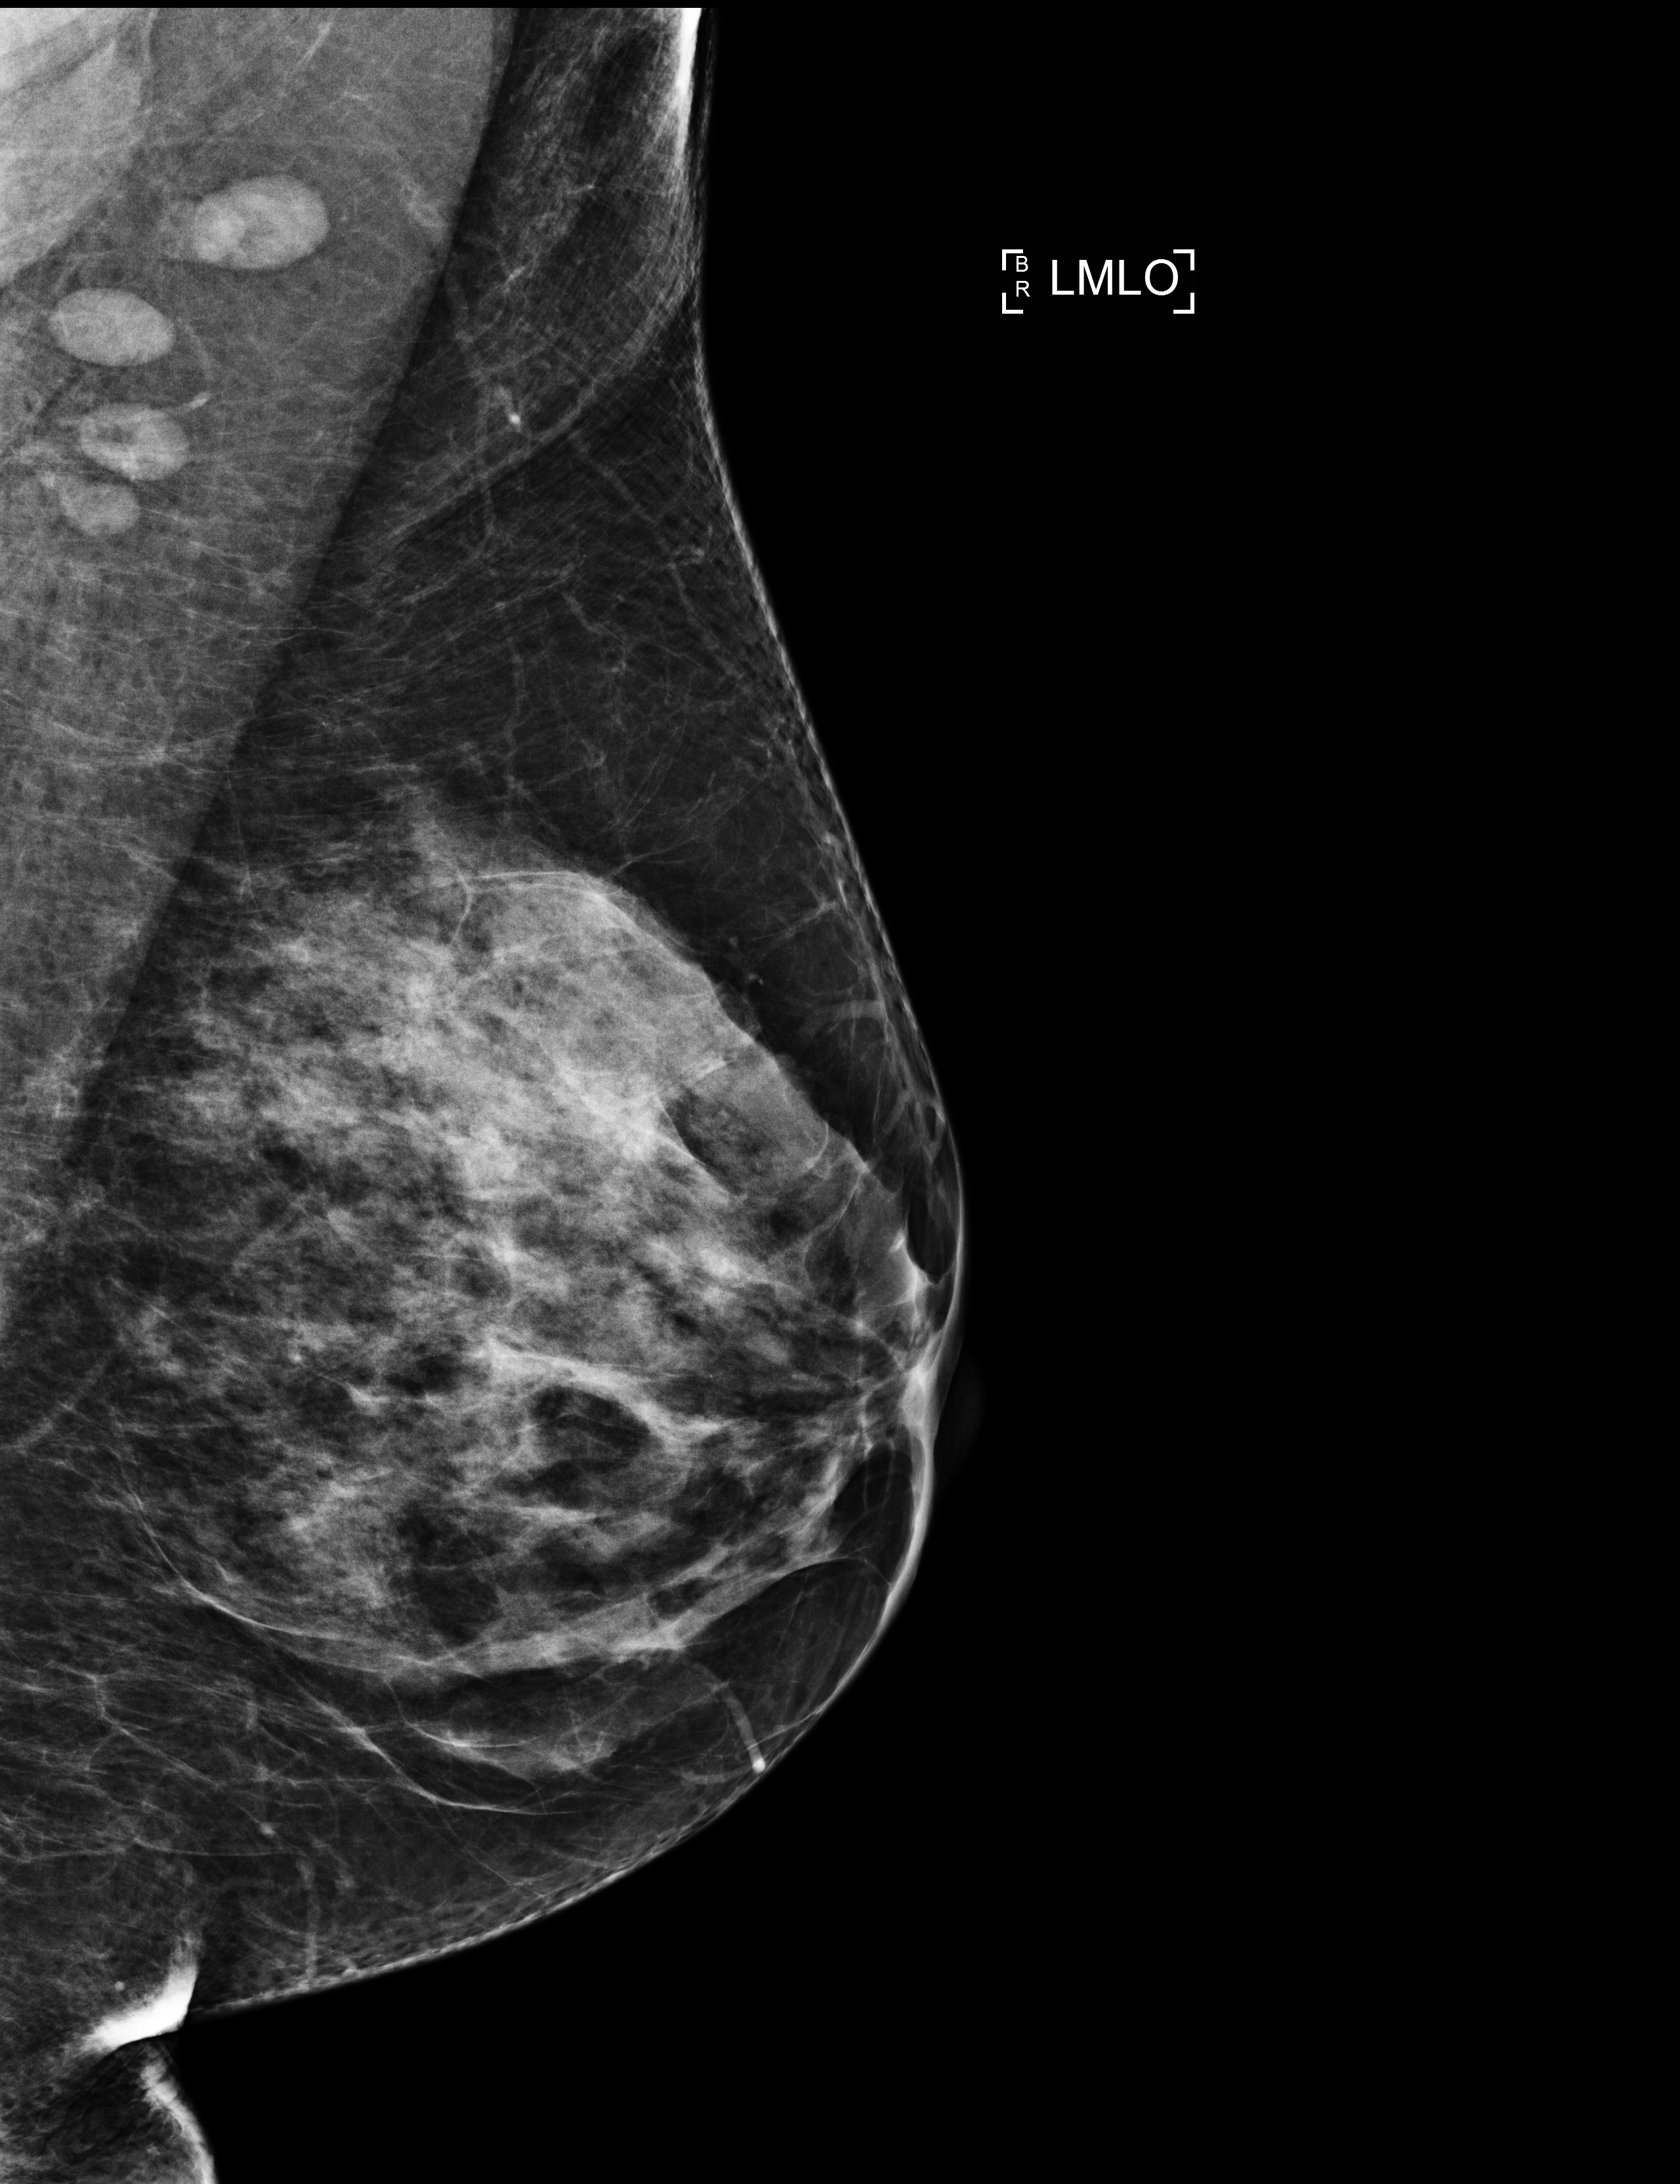
Screening examination; compressed breast thickness 60 mm. Patient aged 67 years (female).
Image type: full-field digital mammogram. Breast: left. Projection: medio-lateral oblique projection.